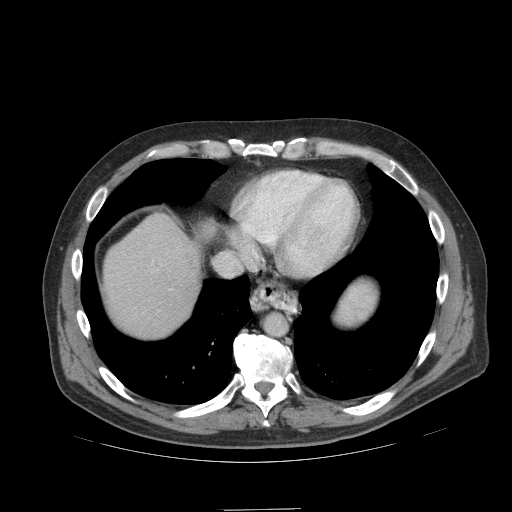
Contrast-enhanced abdominal CT (liver protocol), one axial slice; slice 91 of 99 in the series (ordered by position); reconstruction kernel STANDARD; soft-tissue window (W 400 / L 40 HU); 512 × 512 image matrix. Case-level facts recorded for this patient, not image findings: diagnosis: hepatocellular carcinoma (patient treated with transarterial chemoembolisation; whether this scan precedes or follows treatment is not stated here); TNM stage (as recorded): Stage-I; Child-Pugh class: A.
Annotated regions visible in this slice (semi-automatically segmented with operator editing):
- abdominal aorta: box from (x=264, y=314) to (x=287, y=335) px
- liver parenchyma outside the tumour (the mass and vessels are separate outlines, so this box may not span the whole liver): (x=104, y=214)–(x=212, y=336)